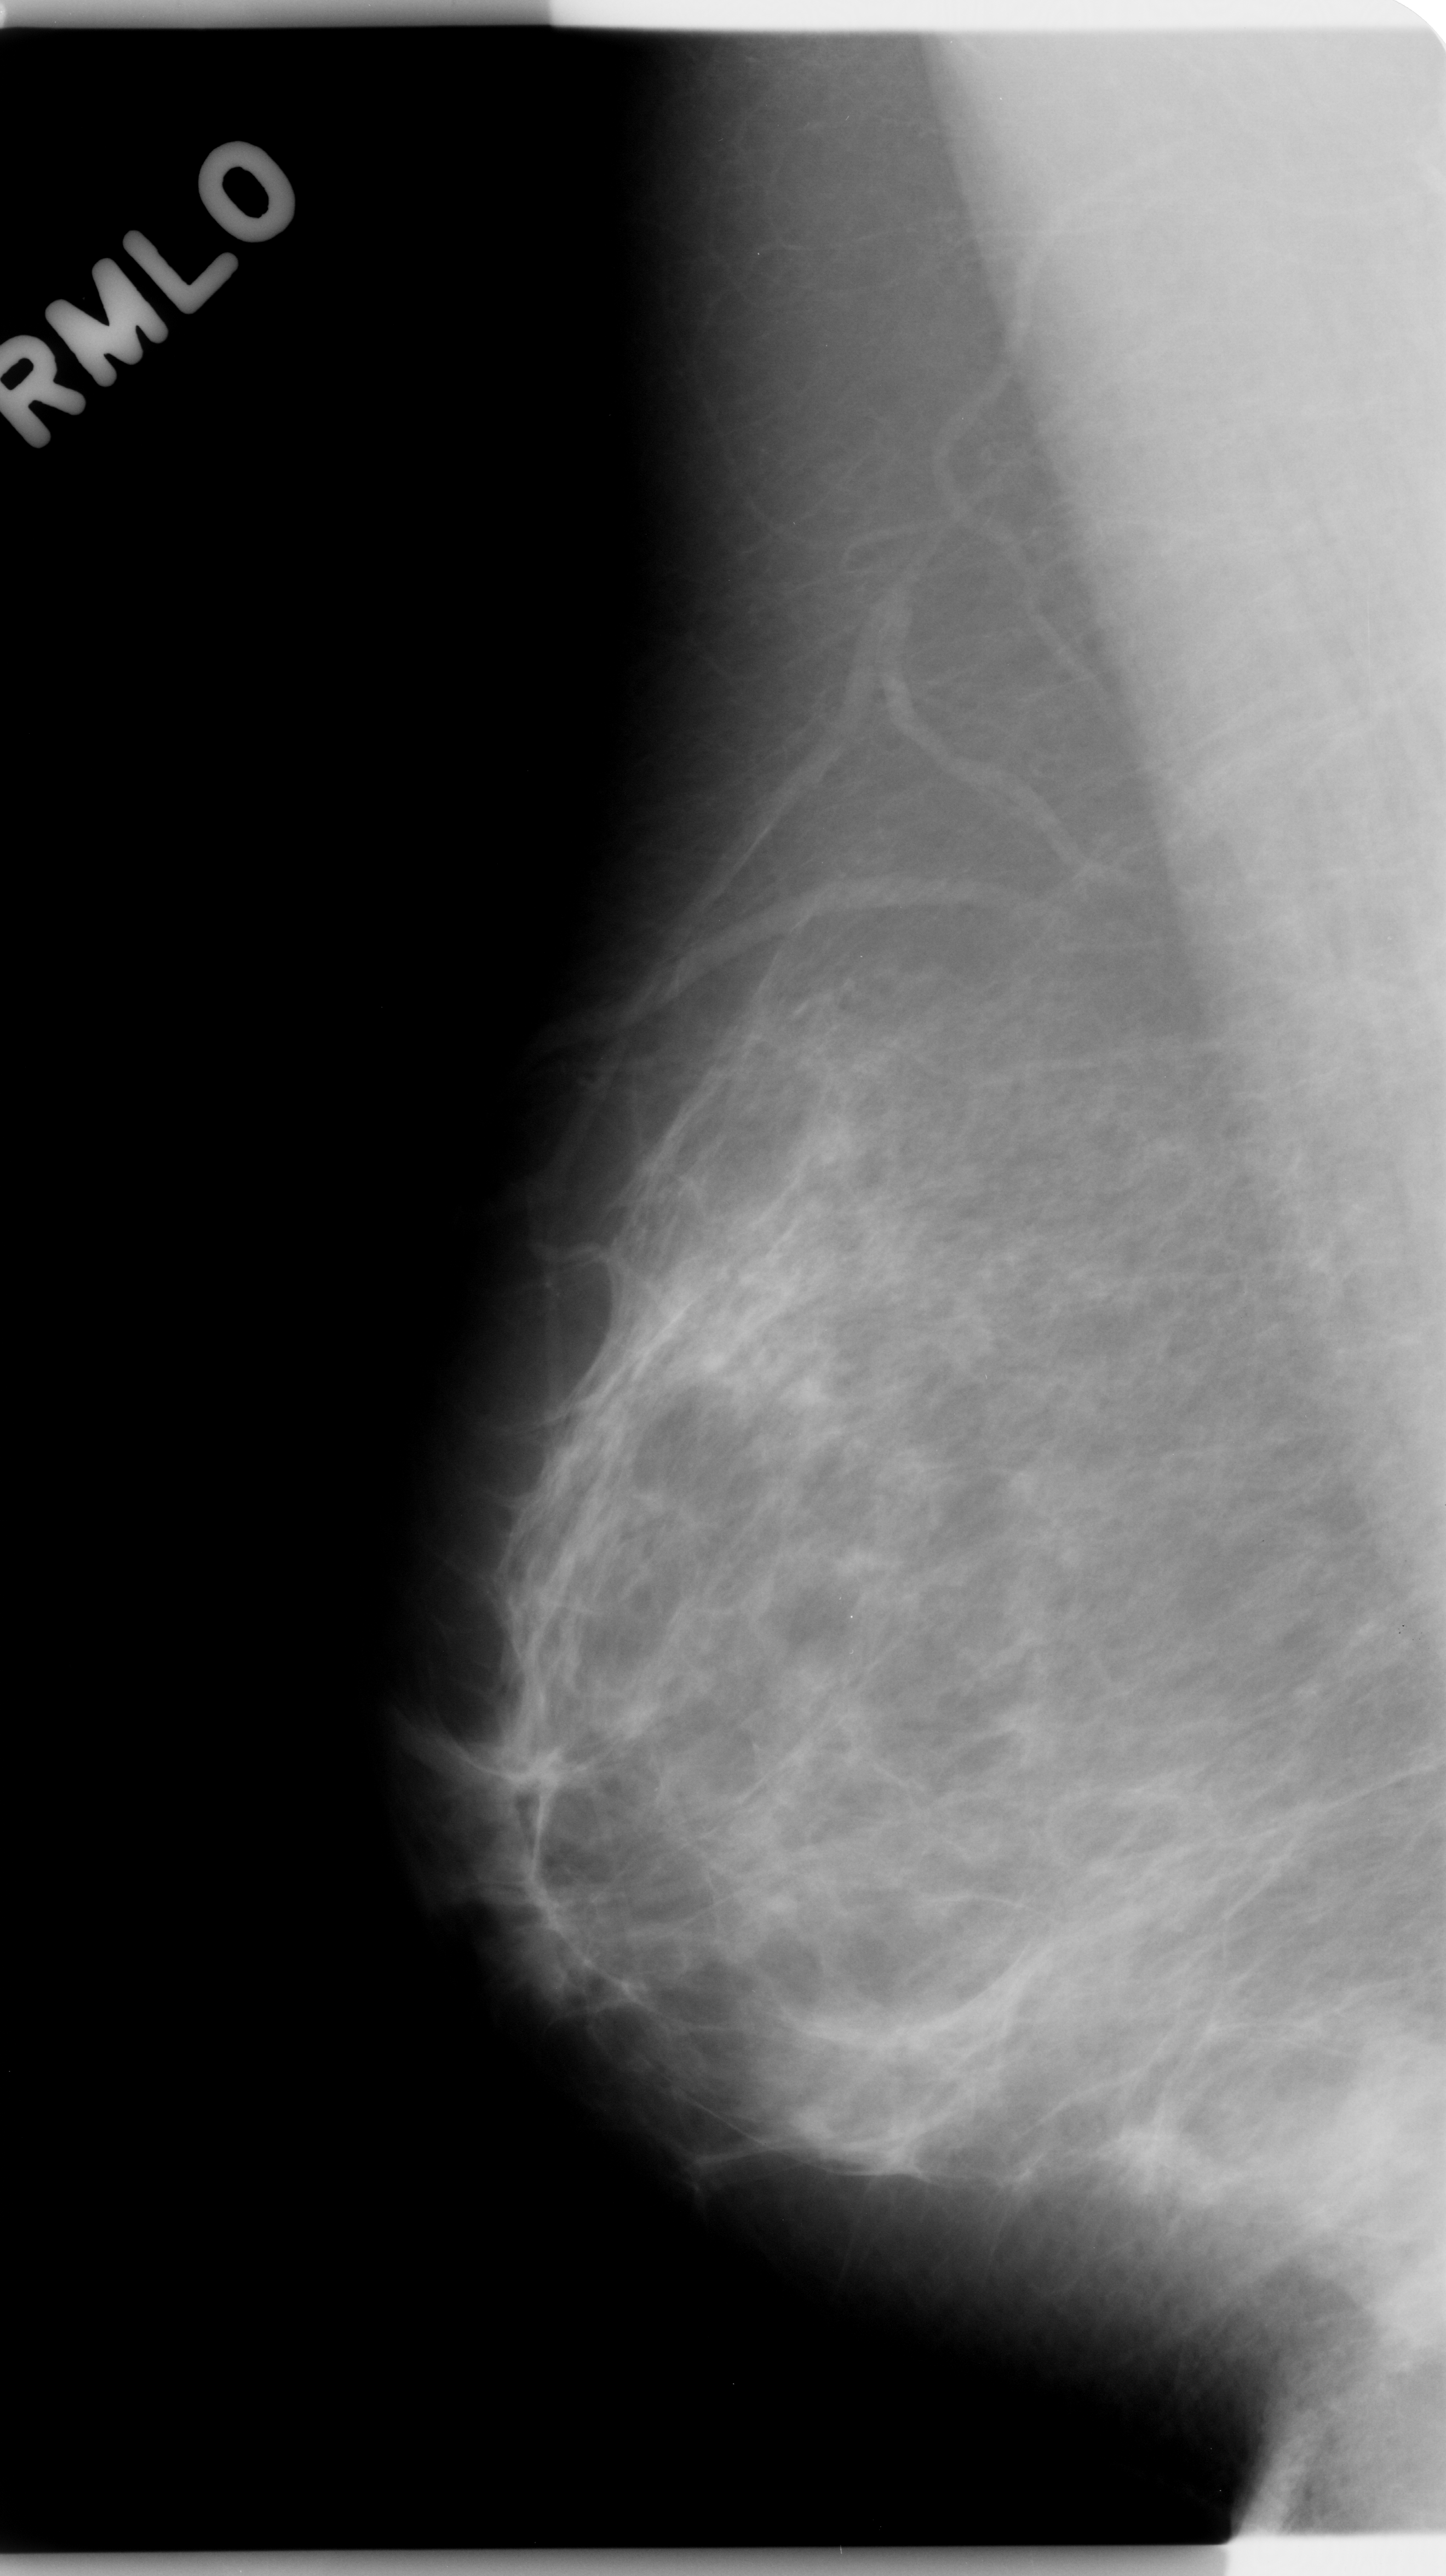
Mammogram (digitized film); right breast; mediolateral oblique (MLO) view; BI-RADS breast density category 2 (scale 1–4).
- Abnormality record for this image: mass, shape irregular, margins ill defined; BI-RADS assessment category 4; pathology (as recorded): benign.